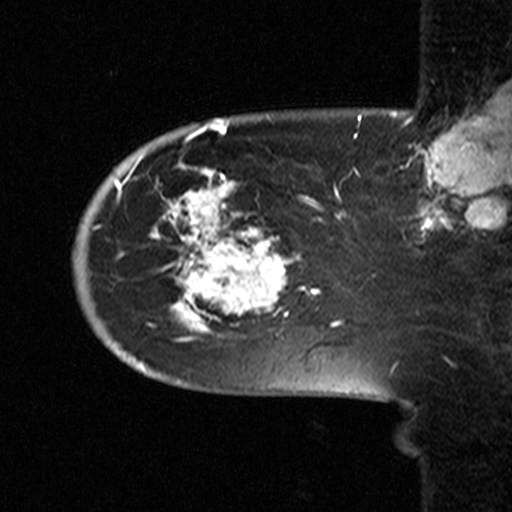
Breast MRI (dynamic contrast-enhanced), one sagittal slice. Position 10 of 44 along the scan axis. Dynamic contrast-enhanced study with each time point stored as its own series, time point 2 of 3 at this slice position (early post-contrast, ordered by acquisition time). 1.5 T. TE 4.5 ms, TR 11 ms. 3.27 mm slice thickness. 512 × 512 image matrix, field of view 200 × 200 mm. Patient: female, 53 years. From the clinical record (not read from this slice): setting: breast cancer imaged before/during neoadjuvant chemotherapy; receptor status: HR-positive, HER2-negative.
Outlined on this slice (semi-automatically segmented with operator editing):
- analysis volume of interest (the breast-tissue region the enhancement analysis was run in; not a lesion): bounding box (x1, y1, x2, y2) in pixels: (68, 154, 311, 367)
- tumour enhancement mask (voxels above the 90 % enhancement threshold inside the analysis volume of interest): (116, 169, 311, 342)